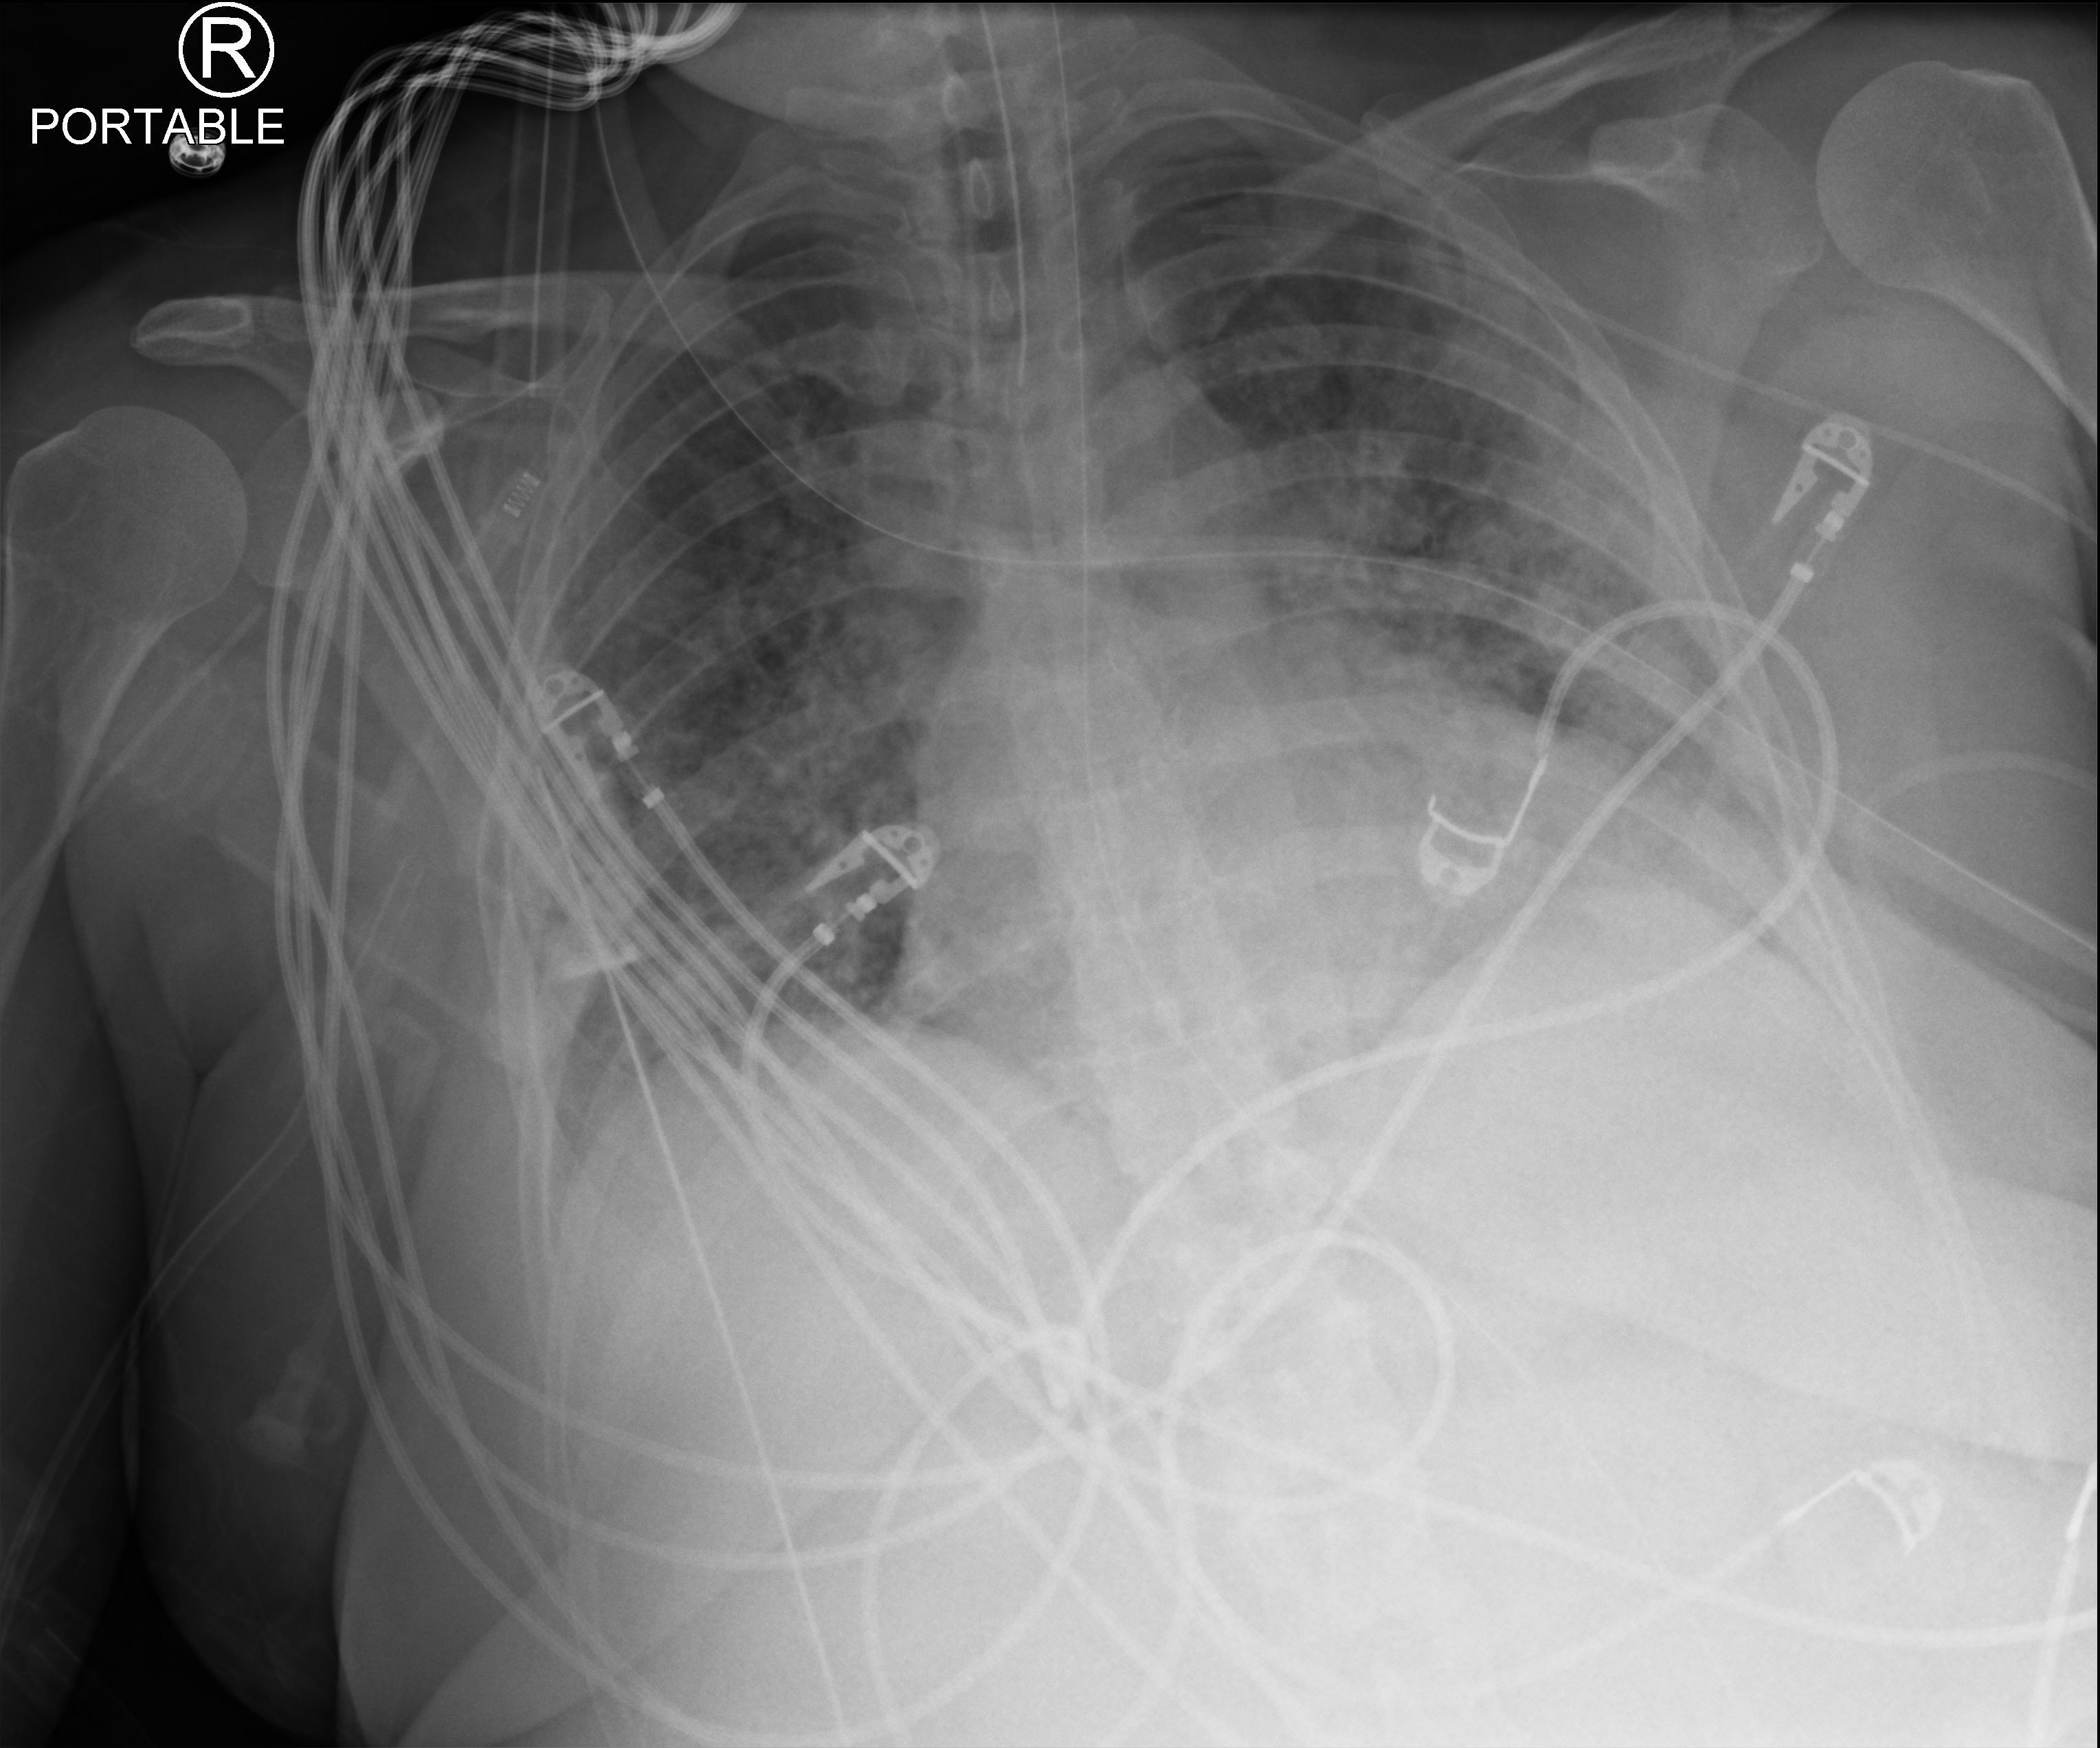
Bedside chest radiograph (computed radiography); anteroposterior (AP) projection. Patient hospitalised with COVID-19; female, aged 18–59 years.
Hospital-stay facts (about this admission, not read from this image; timing relative to this image not recorded): admitted to intensive care during this hospital stay: yes; mechanically ventilated during this hospital stay: yes; diabetes (admission record): yes.